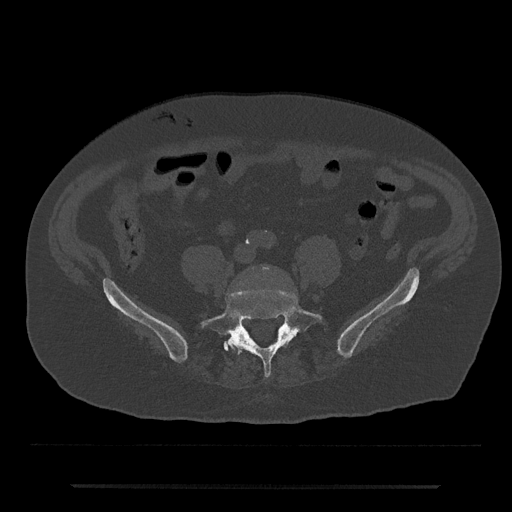
CT including the spine, one axial slice. Position 296 of 797 along the scan axis. Bone window (W 1800 / L 400 HU). 512 × 512 image matrix, field of view 434 × 434 mm. Patient: male, 80 years. From the clinical record (not read from this slice): primary cancer: prostate; vertebrae with lytic lesions (as recorded): L1, T11.
Annotated regions visible in this slice (semi-automatically segmented with operator editing):
- L4 vertebra: bounding box <262,266,268,270> (left, top, right, bottom; pixels)
- L5 vertebra: <201,290,323,378>